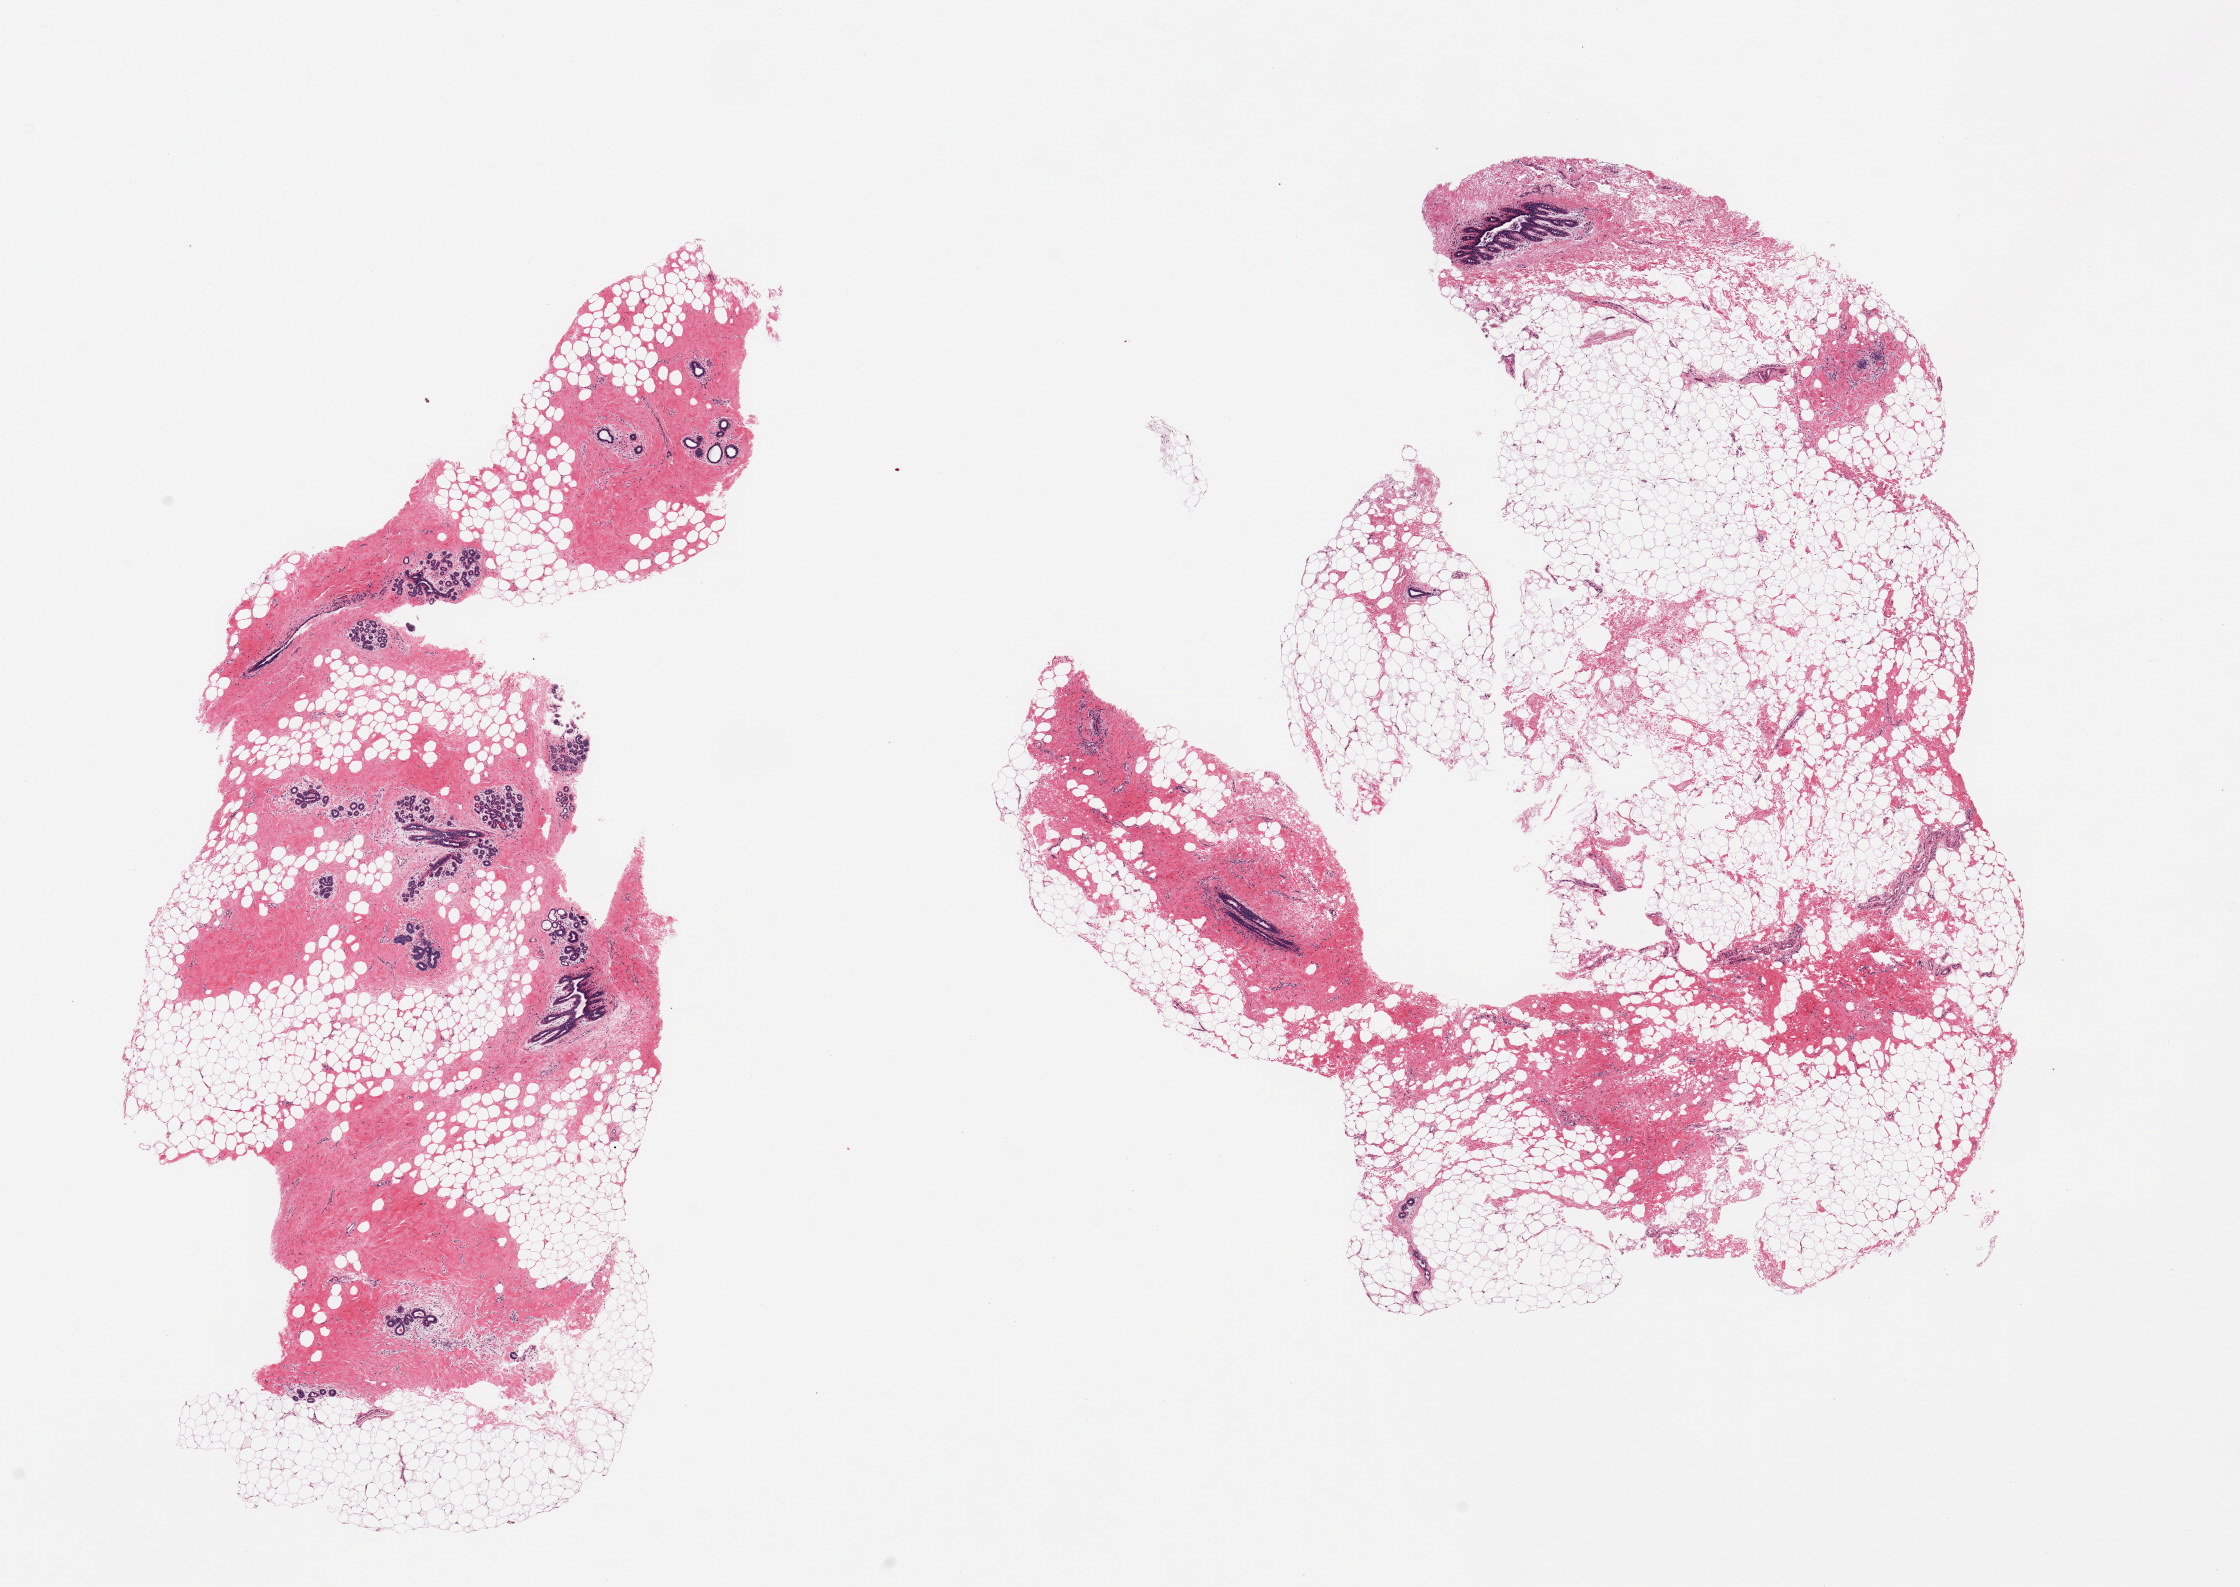
Digitized haematoxylin and eosin-stained section, brightfield, whole scanned area (about 17.7 x 12.6 mm, acquisition: 20x scan) shown as a low-resolution overview; PAXgene-fixed, paraffin-embedded tissue; sampled site (target tissue): breast; donor tissue sample. Female donor.
Review note (as recorded): 2 pieces; fat admixed with stroma with benign ductal/lobular elements.